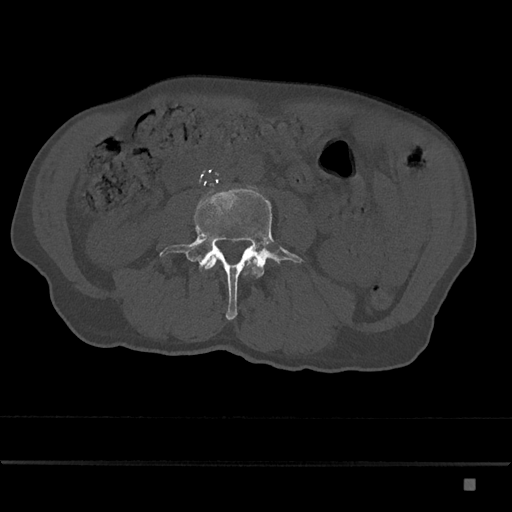
CT including the spine, one axial slice; slice 351 of 797 in the series (ordered by position); reconstruction kernel Br40s/3; bone window (W 1800 / L 400 HU); 512 × 512 image matrix, field of view 390 × 390 mm. Patient: male, 72 years. Case-level facts recorded for this patient, not image findings: primary cancer: prostate.
Structures marked on this image (semi-automatic segmentation, software-assisted and operator-edited):
- L3 vertebra: bounding box [x1, y1, x2, y2] px = [205, 257, 256, 270]
- L4 vertebra: [159, 189, 304, 320]